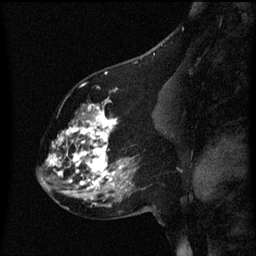
Breast MRI (dynamic contrast-enhanced), one sagittal slice. Position 29 of 60 along the scan axis. Dynamic contrast-enhanced series, image 2 of 3 at this slice position (ordered by acquisition). 1.5 T. TE 4.2 ms, TR 8 ms. 2 mm slice thickness. 256 × 256 image matrix, field of view 200 × 200 mm. Female patient, age 60 years.
Structures marked on this image (semi-automatic segmentation, software-assisted and operator-edited):
- analysis volume of interest (the breast-tissue region the enhancement analysis was run in; not a lesion): bounding box [x1, y1, x2, y2] px = [49, 98, 158, 197]
- tumour enhancement mask (voxels above the 70 % enhancement threshold inside the analysis volume of interest): [49, 100, 130, 195]